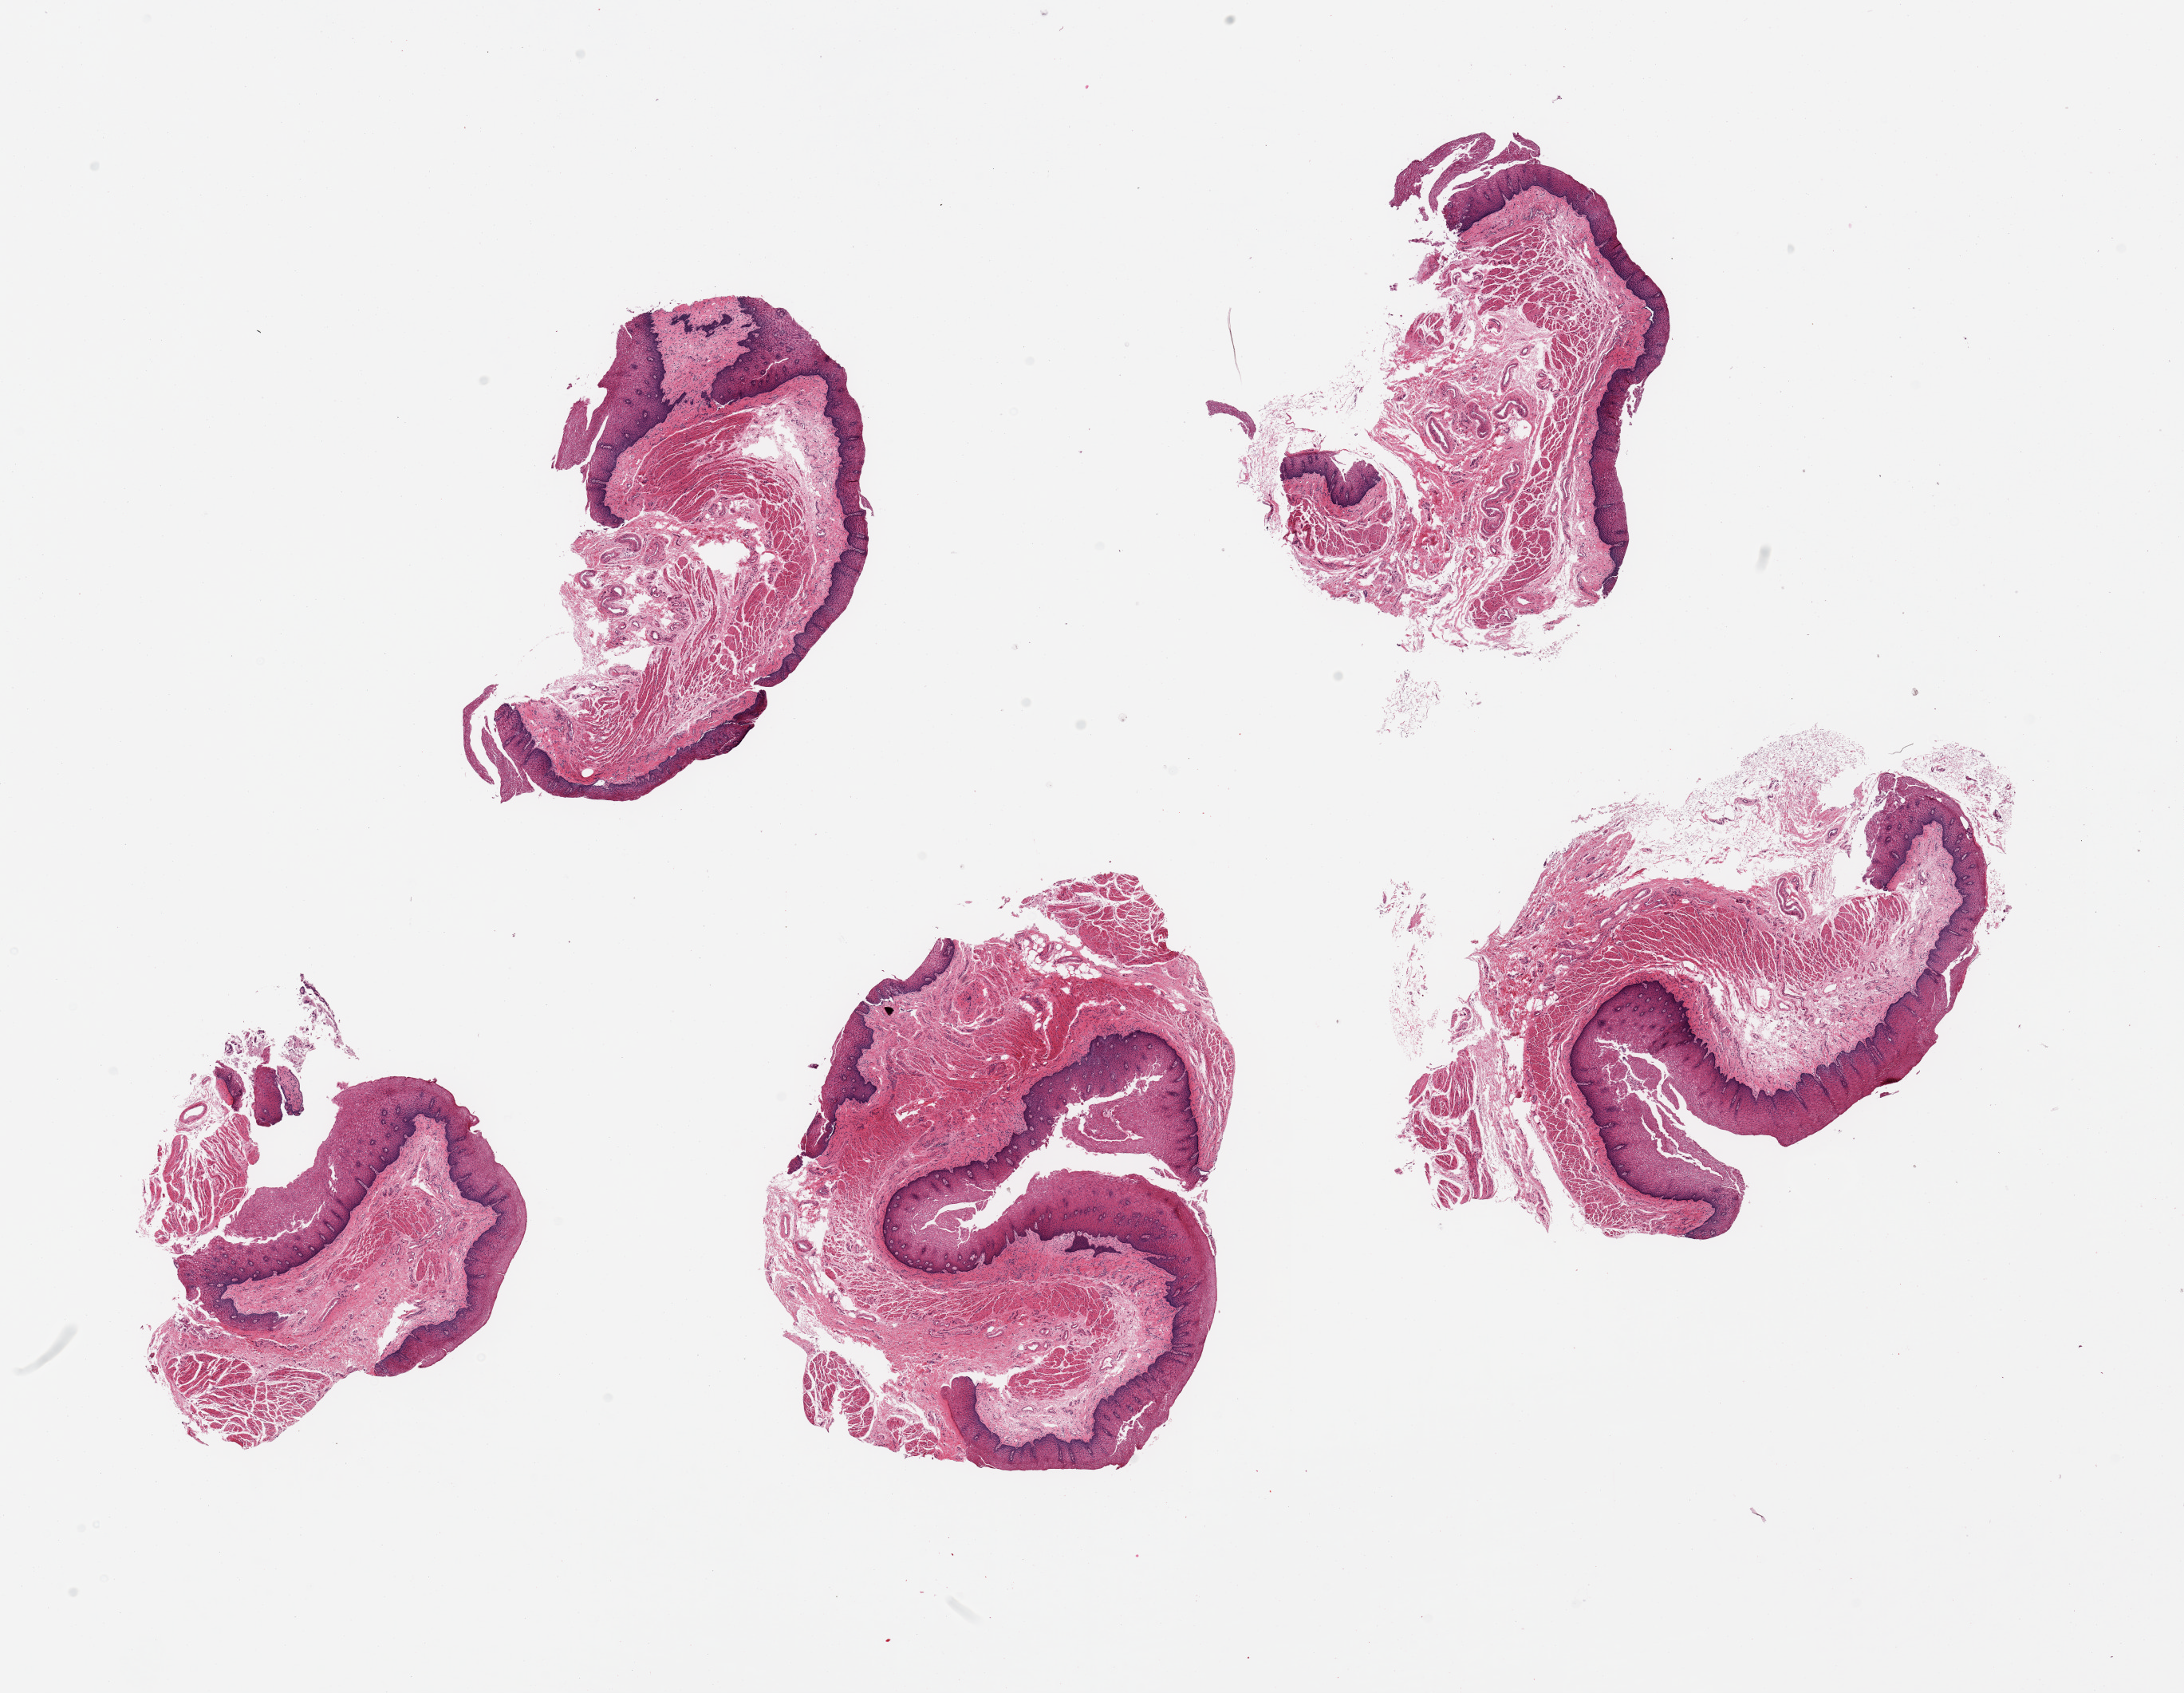
Digitized H&E-stained section, brightfield, shown as a low-resolution overview of the whole scanned area (about 21.7 x 16.8 mm, acquisition: 20x scan); PAXgene-fixed paraffin-embedded (PFPE) section; sampled site (target tissue): esophageal mucous membrane; tissue donor sample. Donor: female.
Review note (as recorded): 5 pieces, squamous mucosa up to~0.4mm.